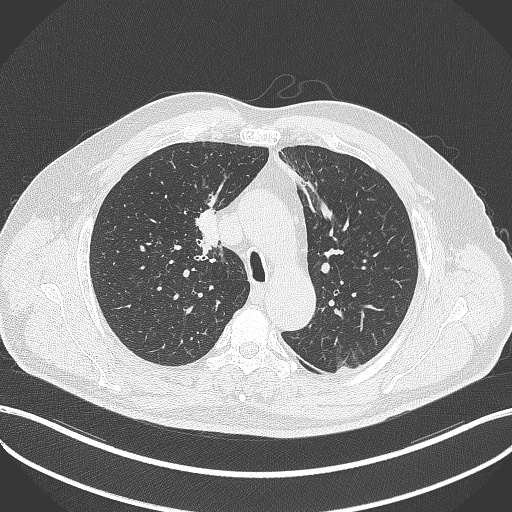
Chest CT, one axial slice; position 274 of 411 along the scan axis; reconstruction kernel B70f; 120 kVp; lung window (W 1500 / L -600 HU); 512 × 512 image matrix, field of view 400 × 400 mm. Patient: male, 60 years. Case-level facts recorded for this patient, not image findings: clinical TNM (as recorded): T1b N1 M0.
Annotated regions visible in this slice (rectangle marked by the reading radiologist):
- lung tumour (recorded histology: squamous cell carcinoma): bounding box (x1, y1, x2, y2) in pixels: (194, 201, 228, 262)